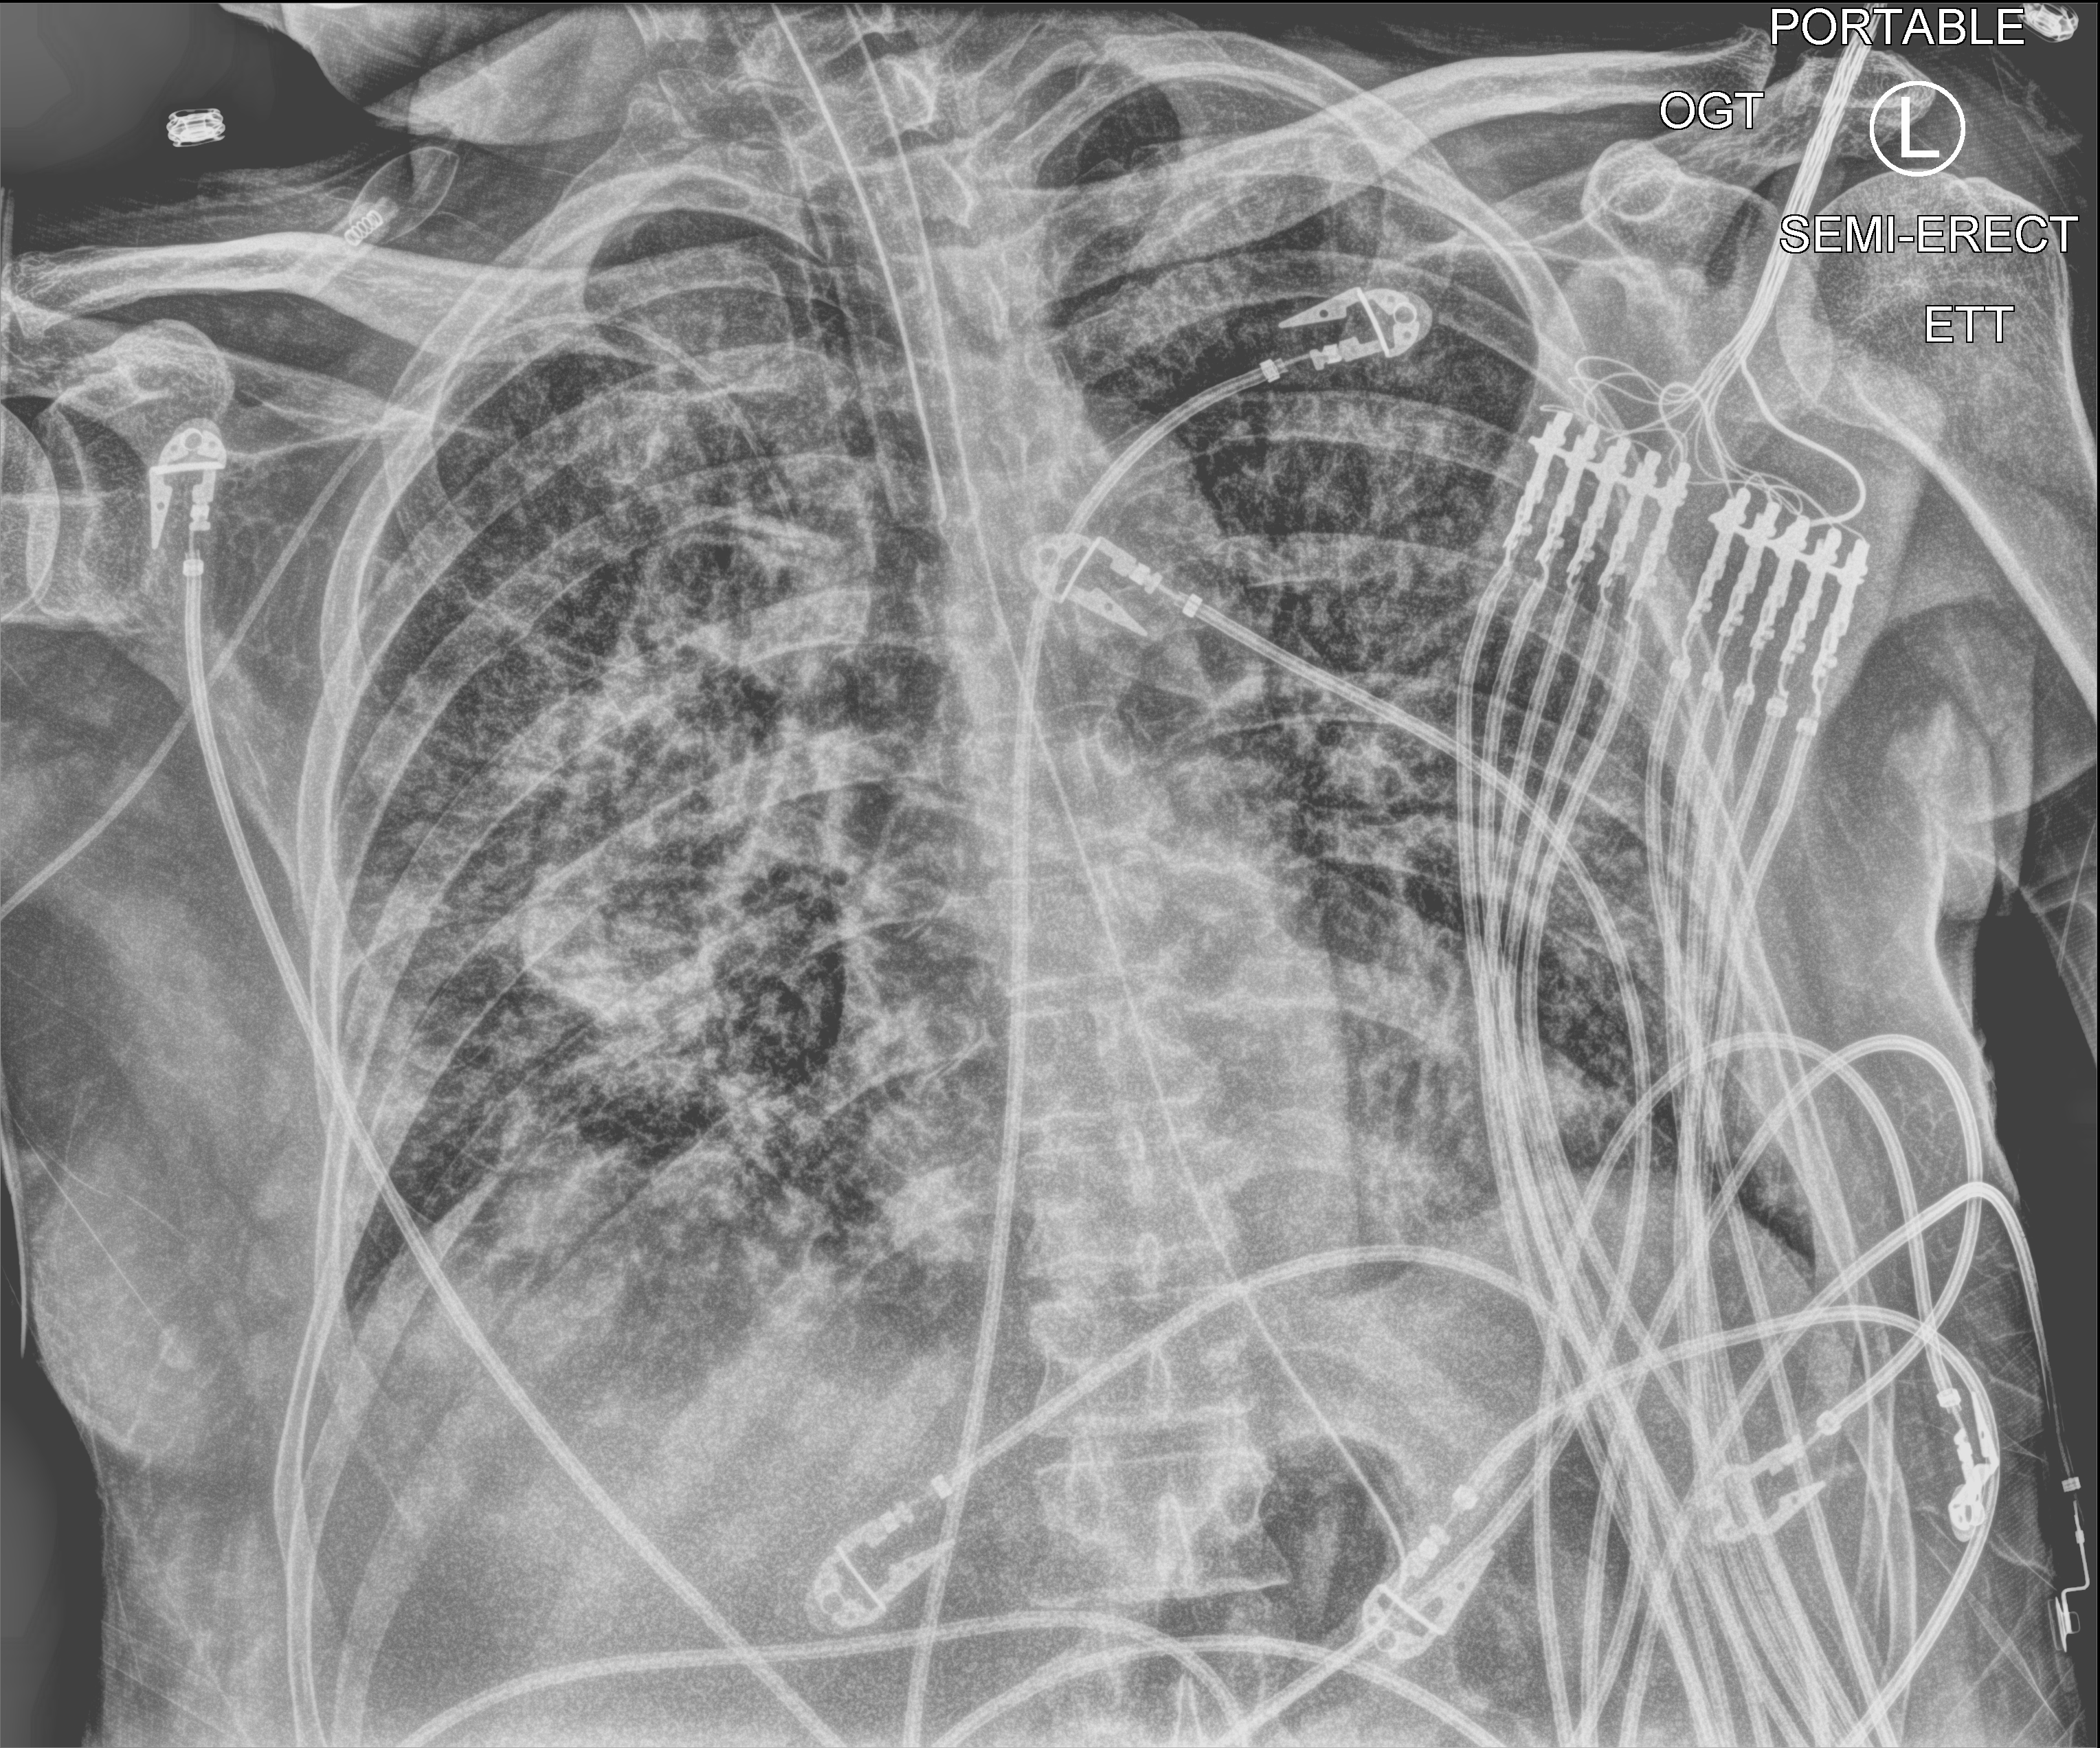
Bedside chest radiograph (computed radiography); anteroposterior (AP) projection. Patient hospitalised with COVID-19; male, aged 60–74 years.
From the hospital-stay record, not from the radiograph (when in the stay this image was taken is not recorded): admitted to intensive care during this hospital stay: yes; mechanically ventilated during this hospital stay: yes; length of hospital stay: 28 days.